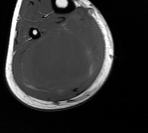
MRI of an extremity soft-tissue mass, one axial slice; MR volume resampled by the dataset authors to the PET/CT grid (not the native acquisition matrix); 148 × 133 image matrix, field of view 145 × 130 mm. Male patient. Case-level facts recorded for this patient, not image findings: histological type: liposarcoma - round cell; grade: high; site of the primary tumour: right calf.
Structures marked on this image (expert contour drawn on MRI and transferred to this co-registered scan by the dataset authors):
- gross tumour volume (mass): bounding box (x1, y1, x2, y2) in pixels: (13, 17, 103, 97)